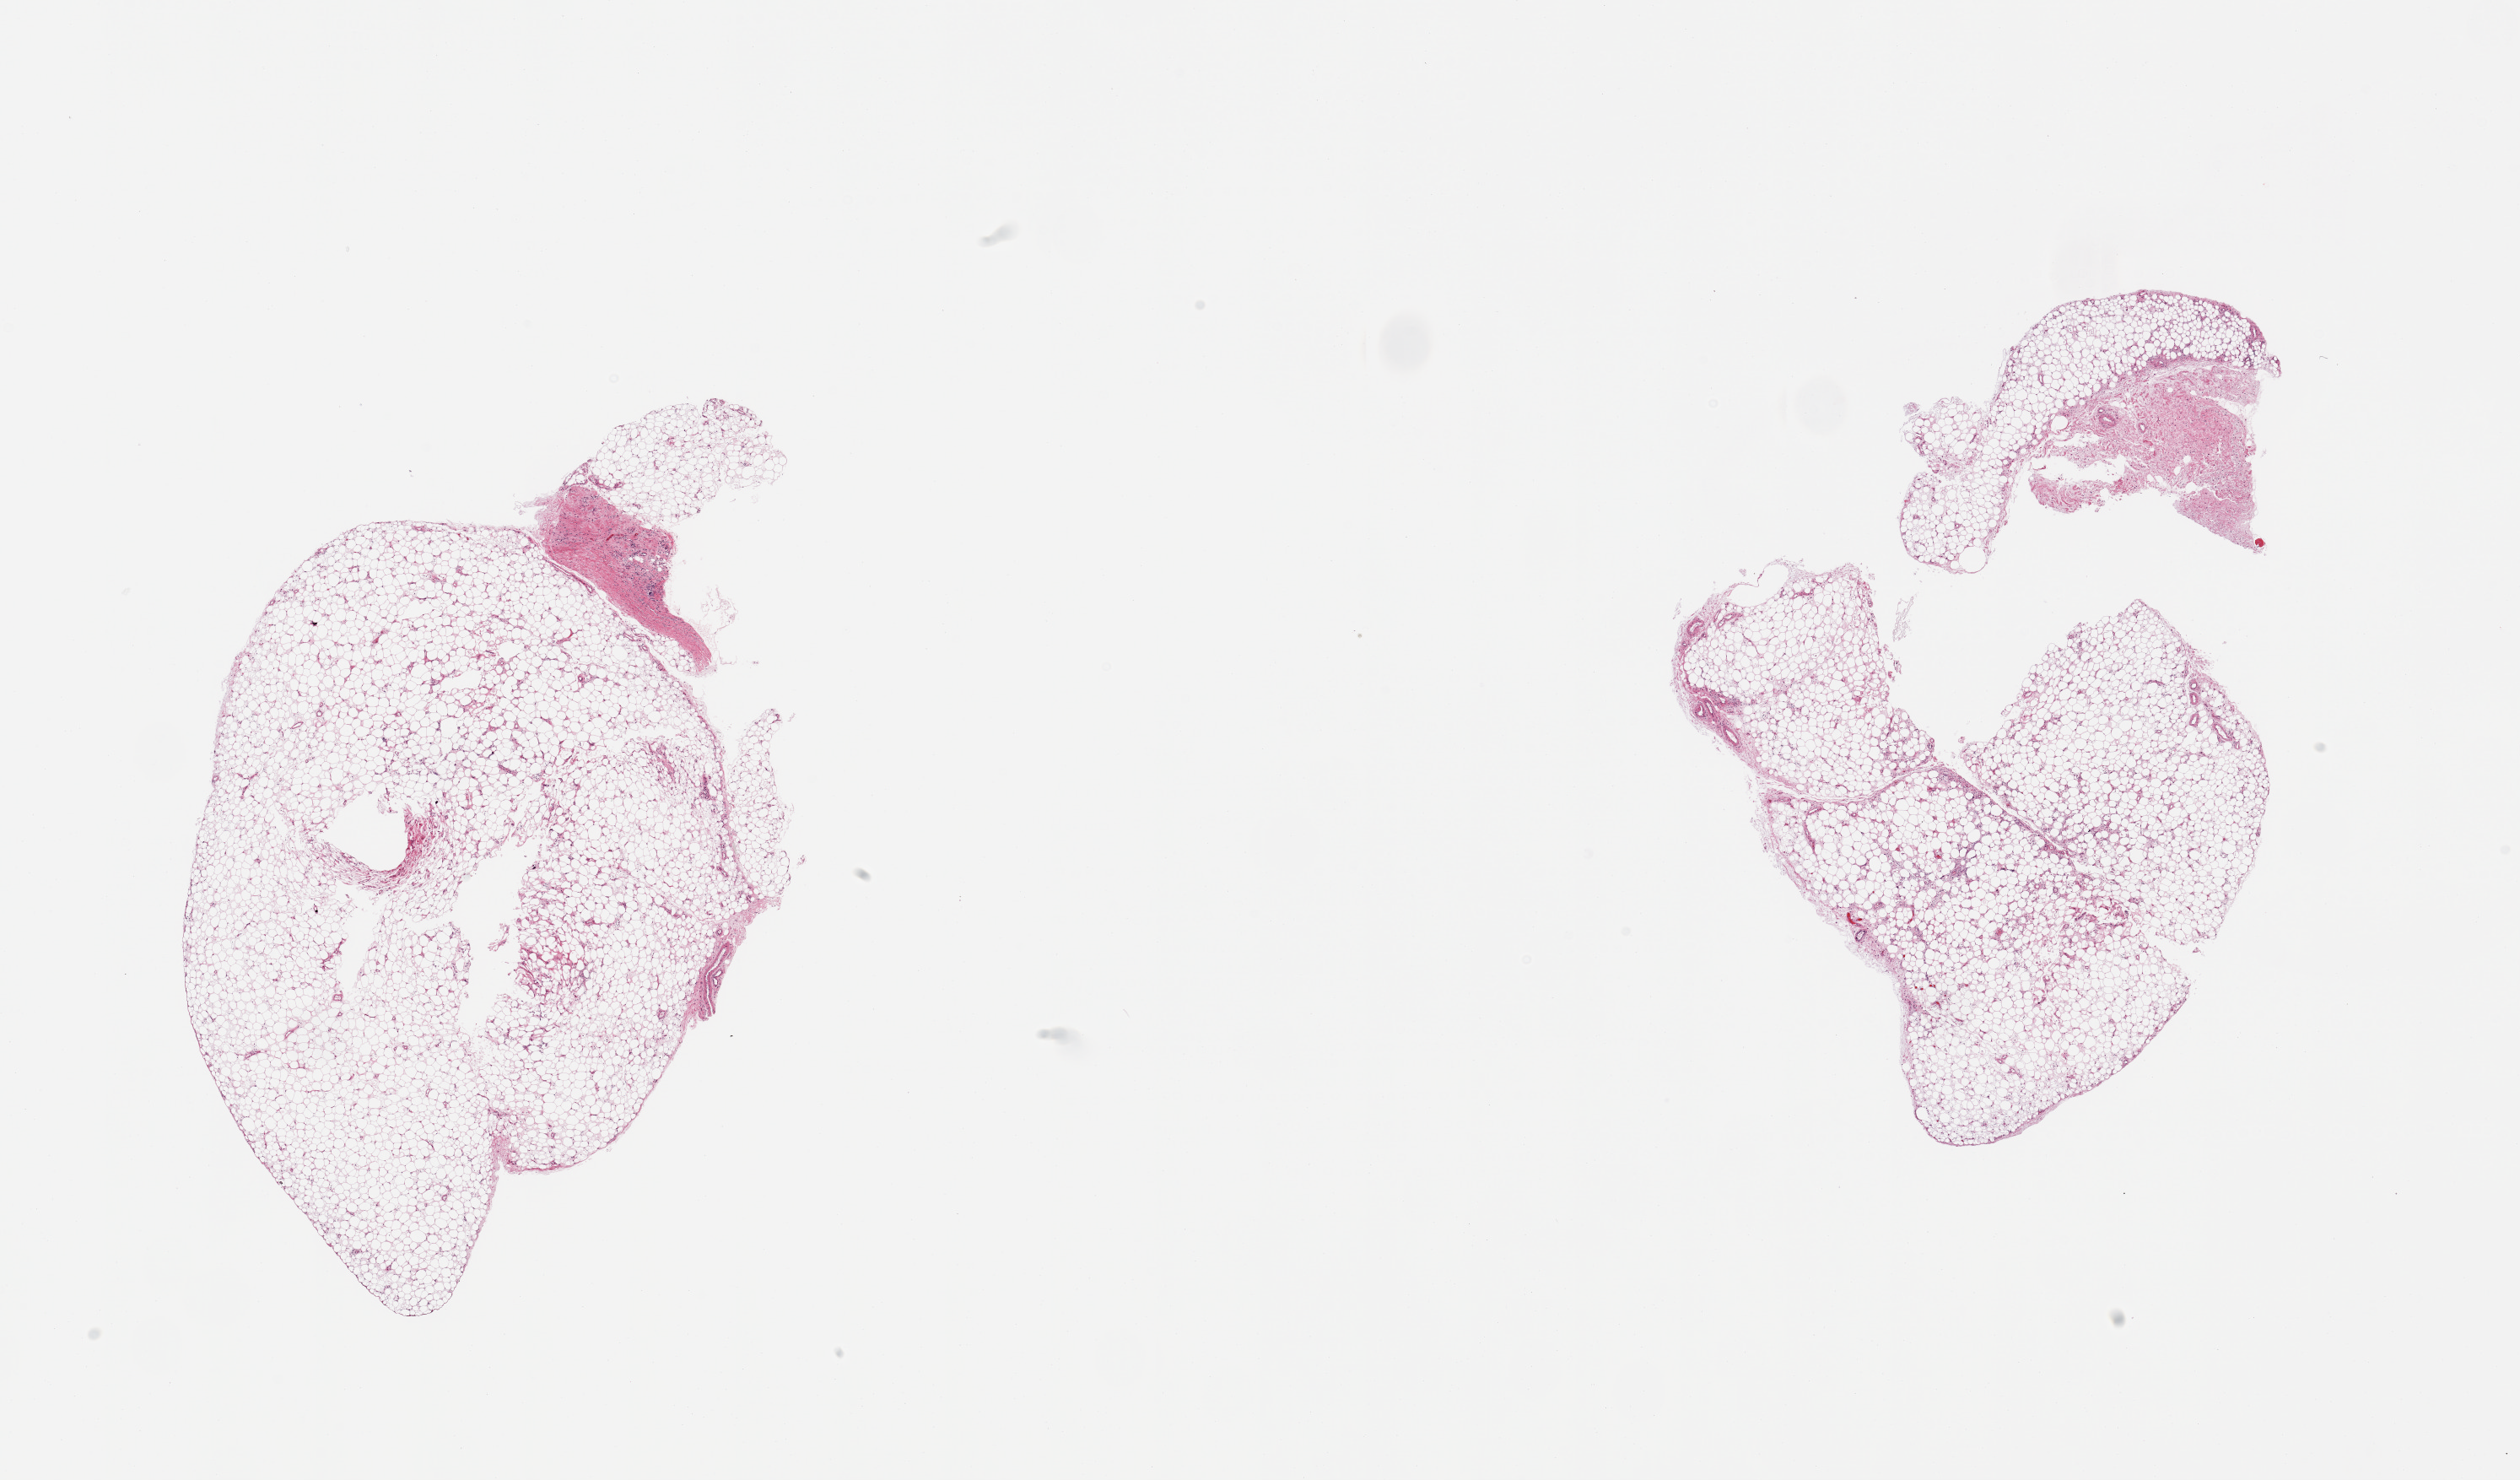
Digitized hematoxylin and eosin (H&E)-stained section, brightfield, a low-resolution overview of the entire scanned area, about 23.6 x 13.9 mm (from a 20x scan); PAXgene-fixed, paraffin-embedded tissue; target tissue: adipose tissue; tissue donor sample. Female donor.
Review note (as recorded): 2 pieces, ~15% fascia/vascular elements.